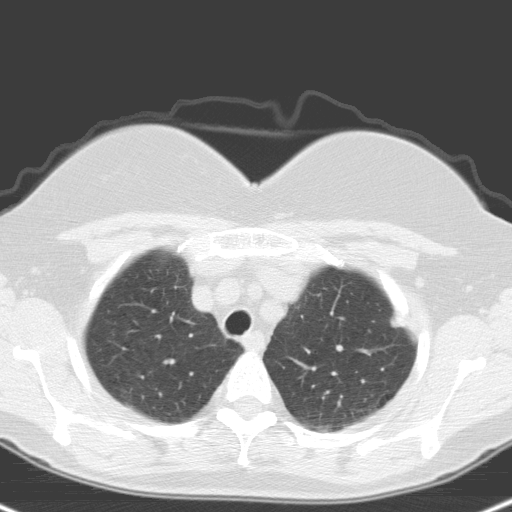
Chest CT (low-dose screening protocol), one axial image; baseline screening round; lung window (W 1500 / L -600 HU); 3.2 mm slice thickness; slice 21 of 148 in the series; 512 × 512 image matrix. Female participant, aged 59 years at enrolment. Current smoker at enrolment.
Lesion marked by an expert reader, bounding box [x1, y1, x2, y2] px = [379, 302, 420, 346]. The screening reader recorded 2 non-calcified nodules or masses ≥4 mm on this exam; which of them this box marks is not recorded. Official screen result: positive, change unspecified: nodule(s) >= 4 mm or enlarging nodule(s), mass(es), or other non-specific abnormalities suspicious for lung cancer. Participant outcome: lung cancer diagnosed 48 days after this screen — large cell neuroendocrine carcinoma, left upper lobe, poorly differentiated (G3), stage IA (AJCC 6th edition), 12 mm at pathology.